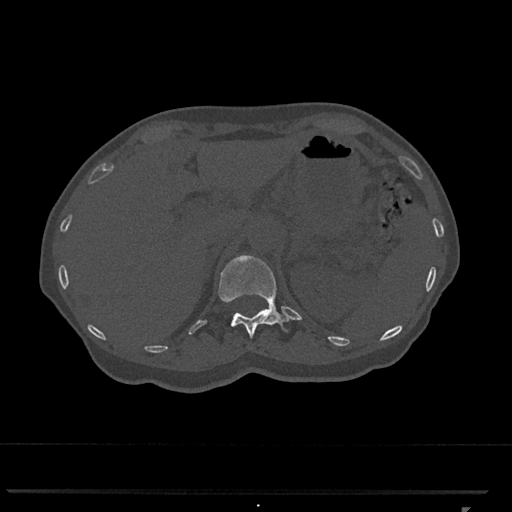
CT including the spine, one axial slice; position 456 of 793 along the scan axis; 120 kVp; bone window (W 1800 / L 400 HU); 0.5 mm slice thickness; 512 × 512 image matrix, field of view 380 × 380 mm. Patient: female, 62 years. From the clinical record (not read from this slice): primary cancer: renal.
Annotated regions visible in this slice (semi-automatically segmented with operator editing):
- T12 vertebra: bounding box (x1, y1, x2, y2) in pixels: (218, 255, 290, 338)